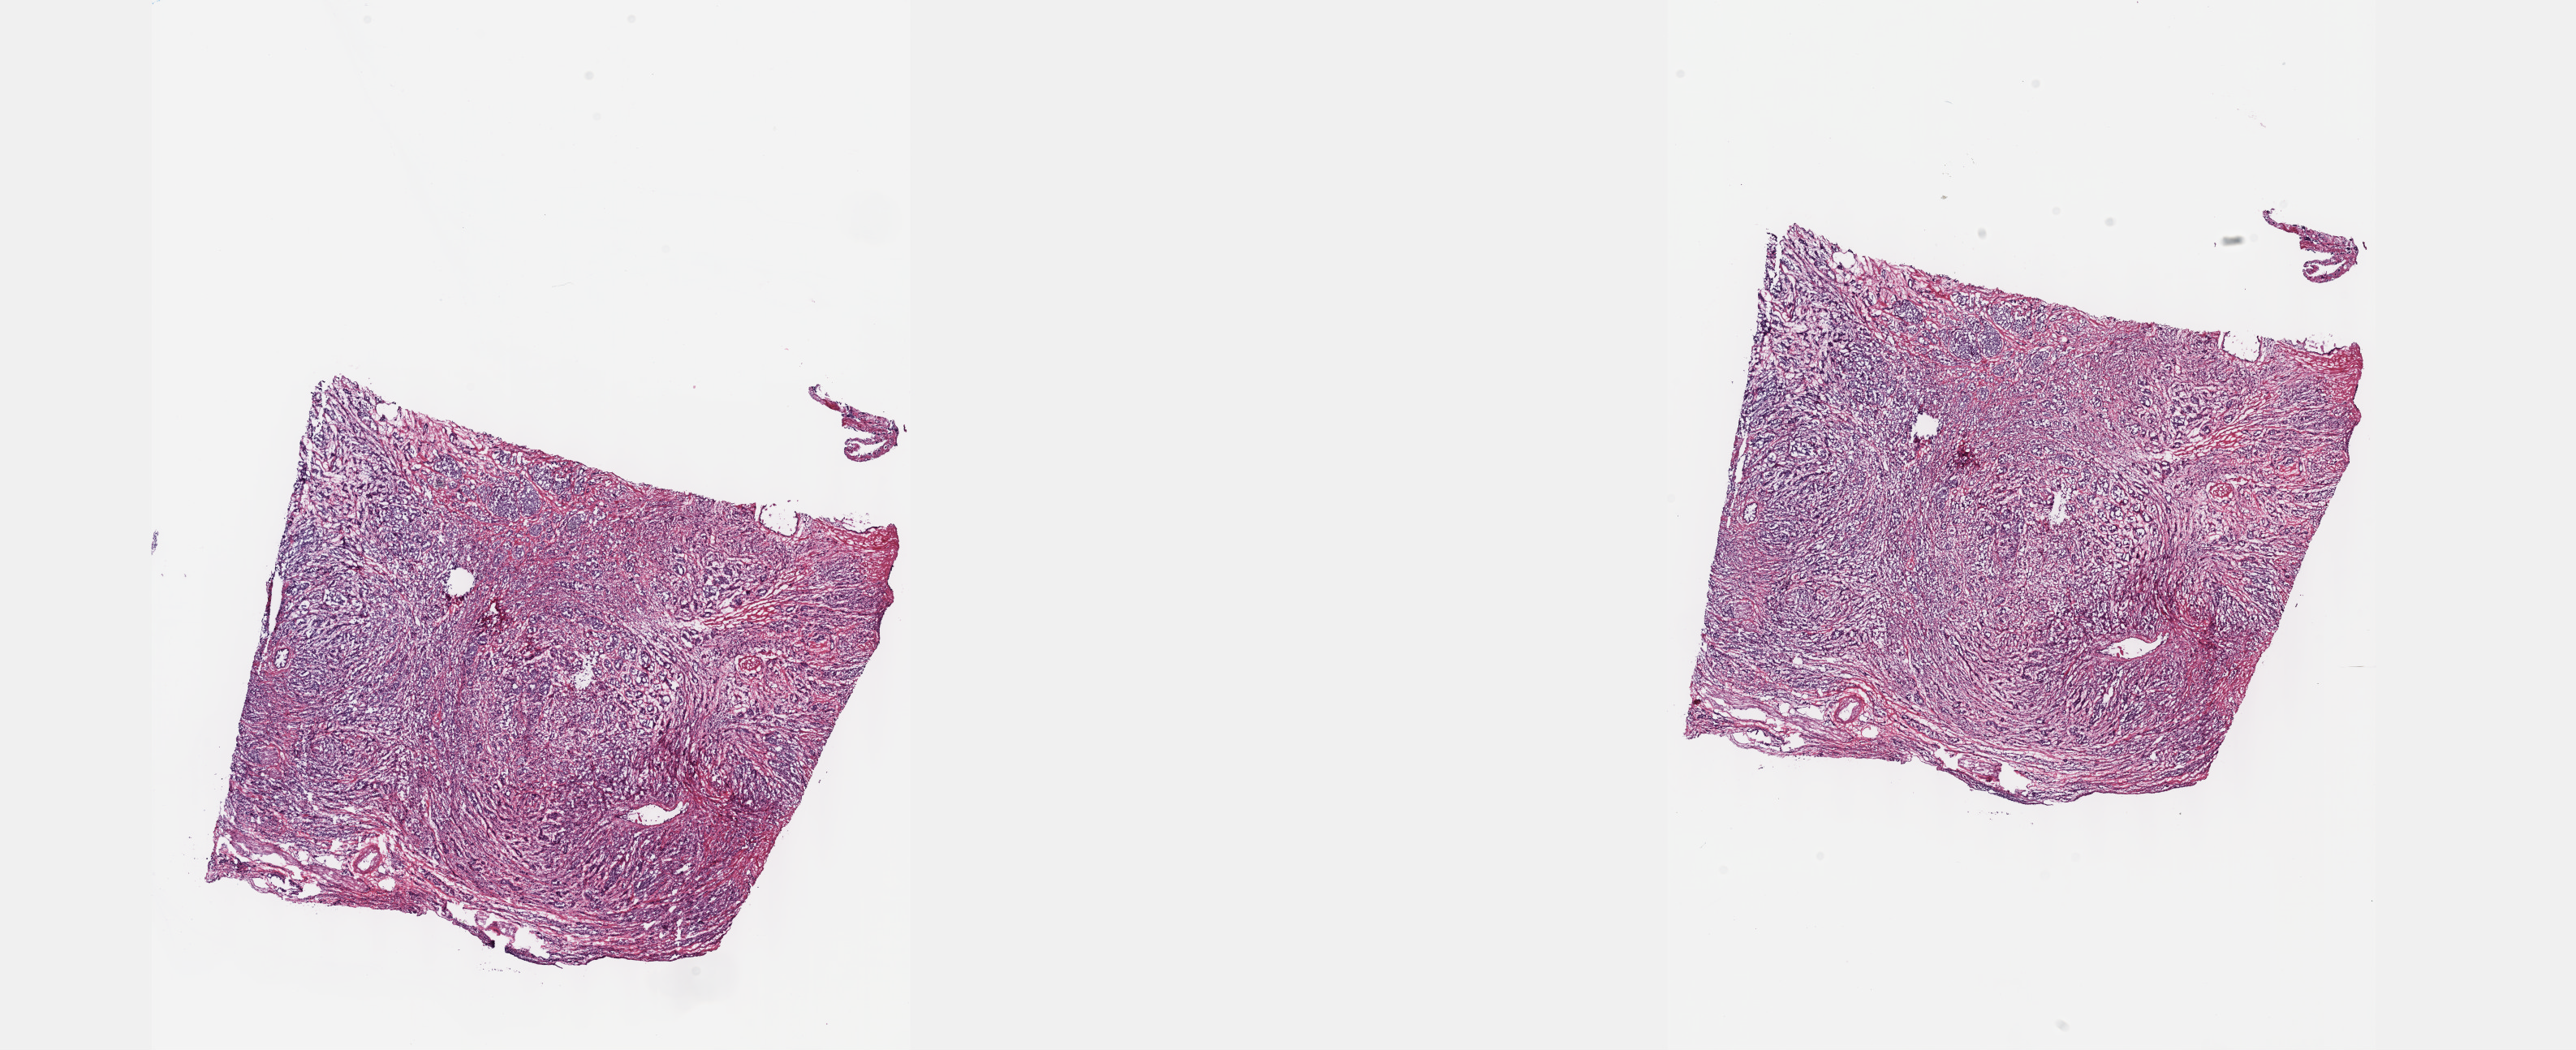
H&E-stained whole-slide image, shown as a low-resolution overview of the whole scanned area (about 25.7 x 10.5 mm, acquisition: 40x scan); frozen section from the top of the tissue portion; sample: primary tumour, prostate. Patient: male, age at initial diagnosis 63 years. Gleason score: 9 (4+5). Slide review estimates, as recorded: tumour cells 90%, tumour nuclei 90%, normal cells 0%, stromal cells 10%, necrosis 0%. Infiltration values recorded for this section: lymphocyte infiltration 40%, monocyte infiltration 20%, neutrophil infiltration 20%.
• lymph nodes positive (case pathology): 0 of 1 examined
• laterality: bilateral
• histologic diagnosis: Adenocarcinoma, NOS (prostate gland)